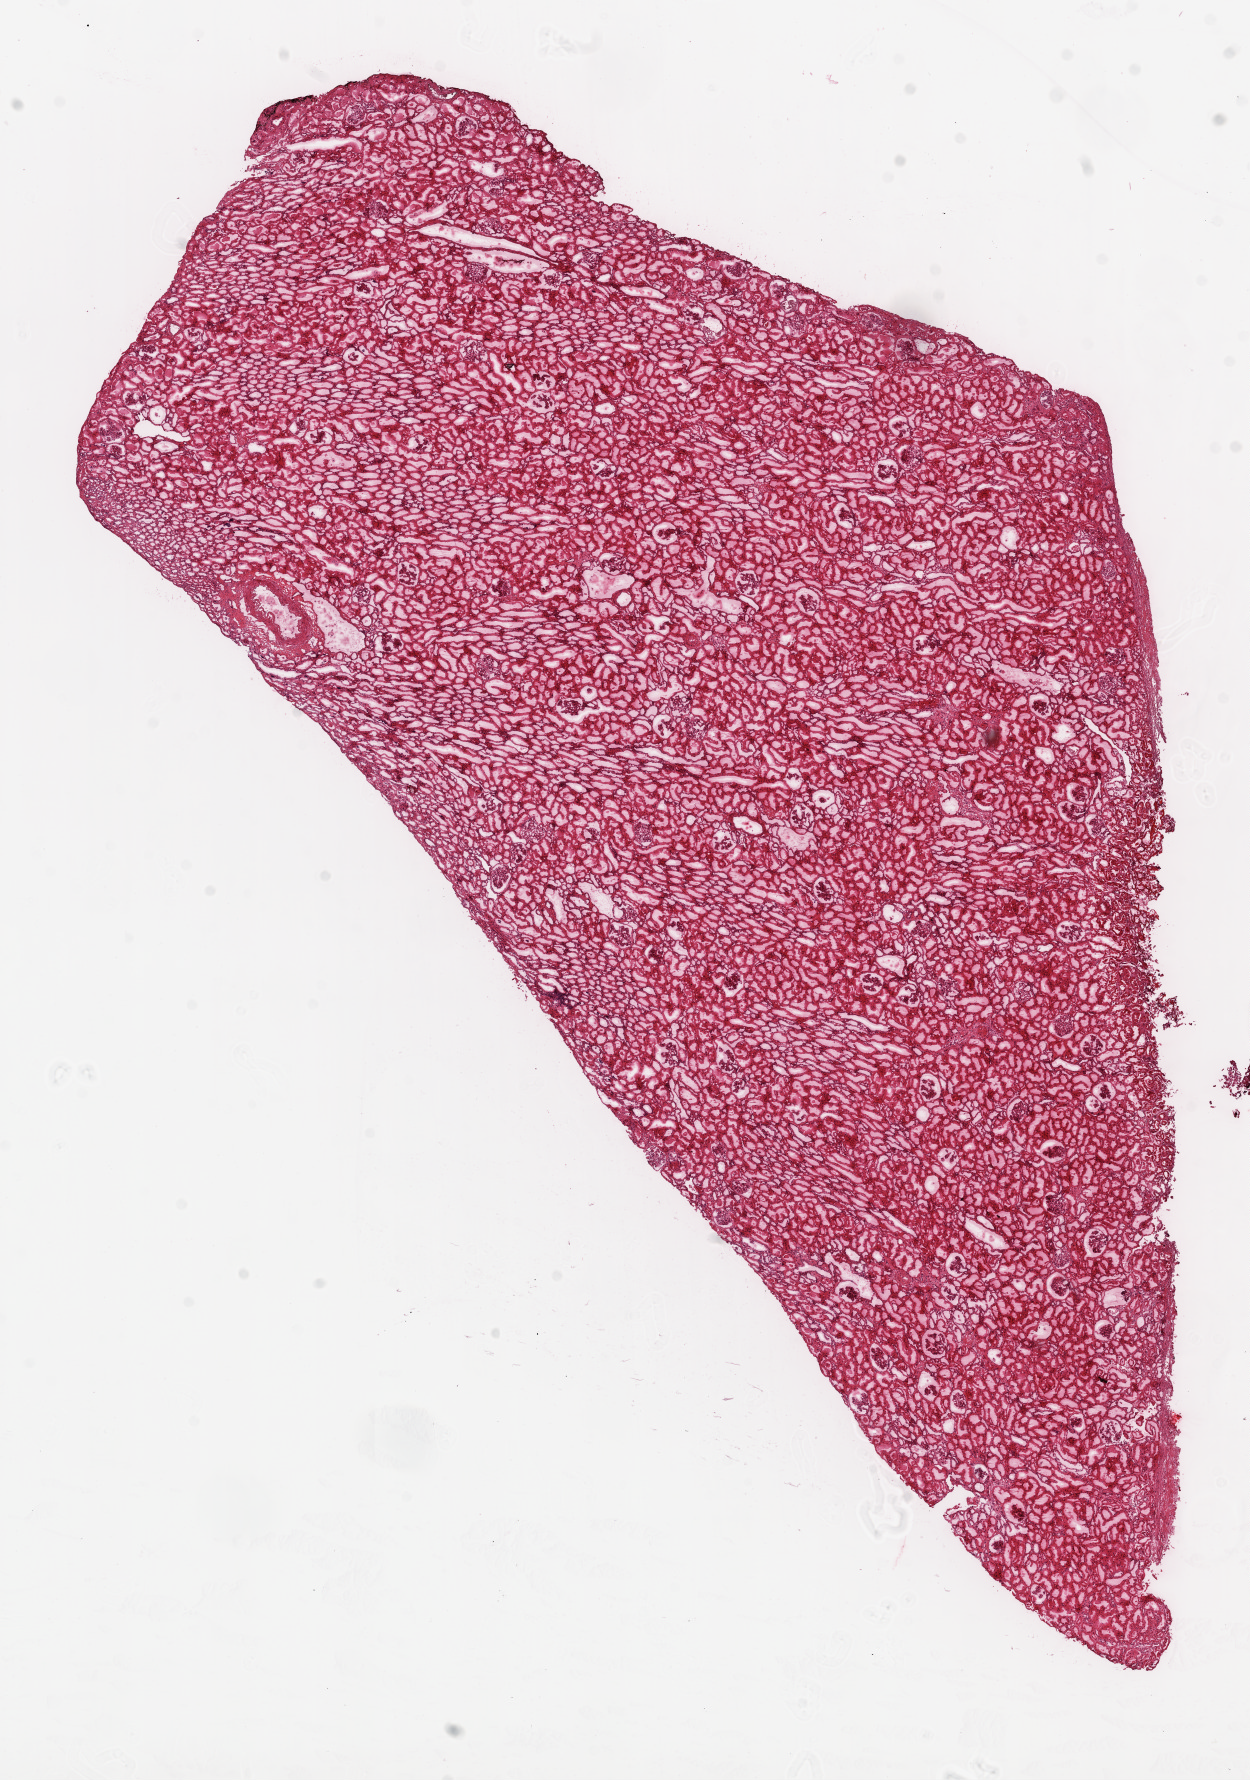
Digitized H&E tissue section (whole slide) — a low-resolution overview of the entire scanned area, about 10.0 x 14.3 mm; frozen section from the top of the tissue portion; sample: solid tissue normal (non-tumour tissue), kidney. Patient: female, age at initial diagnosis 50 years.
This section: solid tissue normal (non-tumour) sample from the same patient. Patient diagnosis: Clear cell adenocarcinoma, NOS.